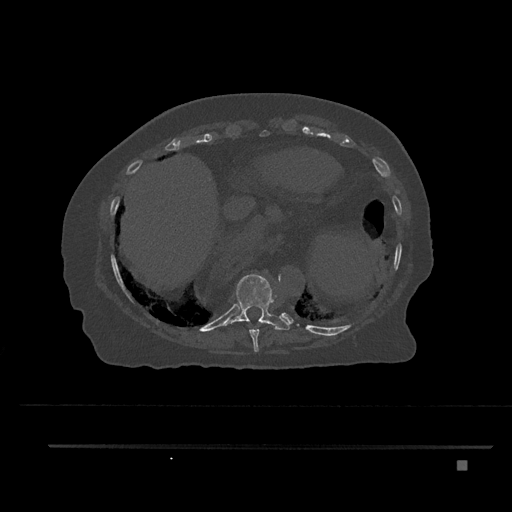
CT including the spine, one axial slice. Reconstruction kernel Br40s/3. 120 kVp. Bone window (W 1800 / L 400 HU). 0.5 mm slice thickness. 512 × 512 image matrix, field of view 437 × 437 mm. Female patient, age 76 years. From the clinical record (not read from this slice): primary cancer: lung; vertebrae with lytic lesions (as recorded): T11, L3.
Structures marked on this image (semi-automatically segmented with operator editing):
- T10 vertebra: box from (x=221, y=274) to (x=290, y=330) px
- T9 vertebra: (x=249, y=320)–(x=263, y=352)